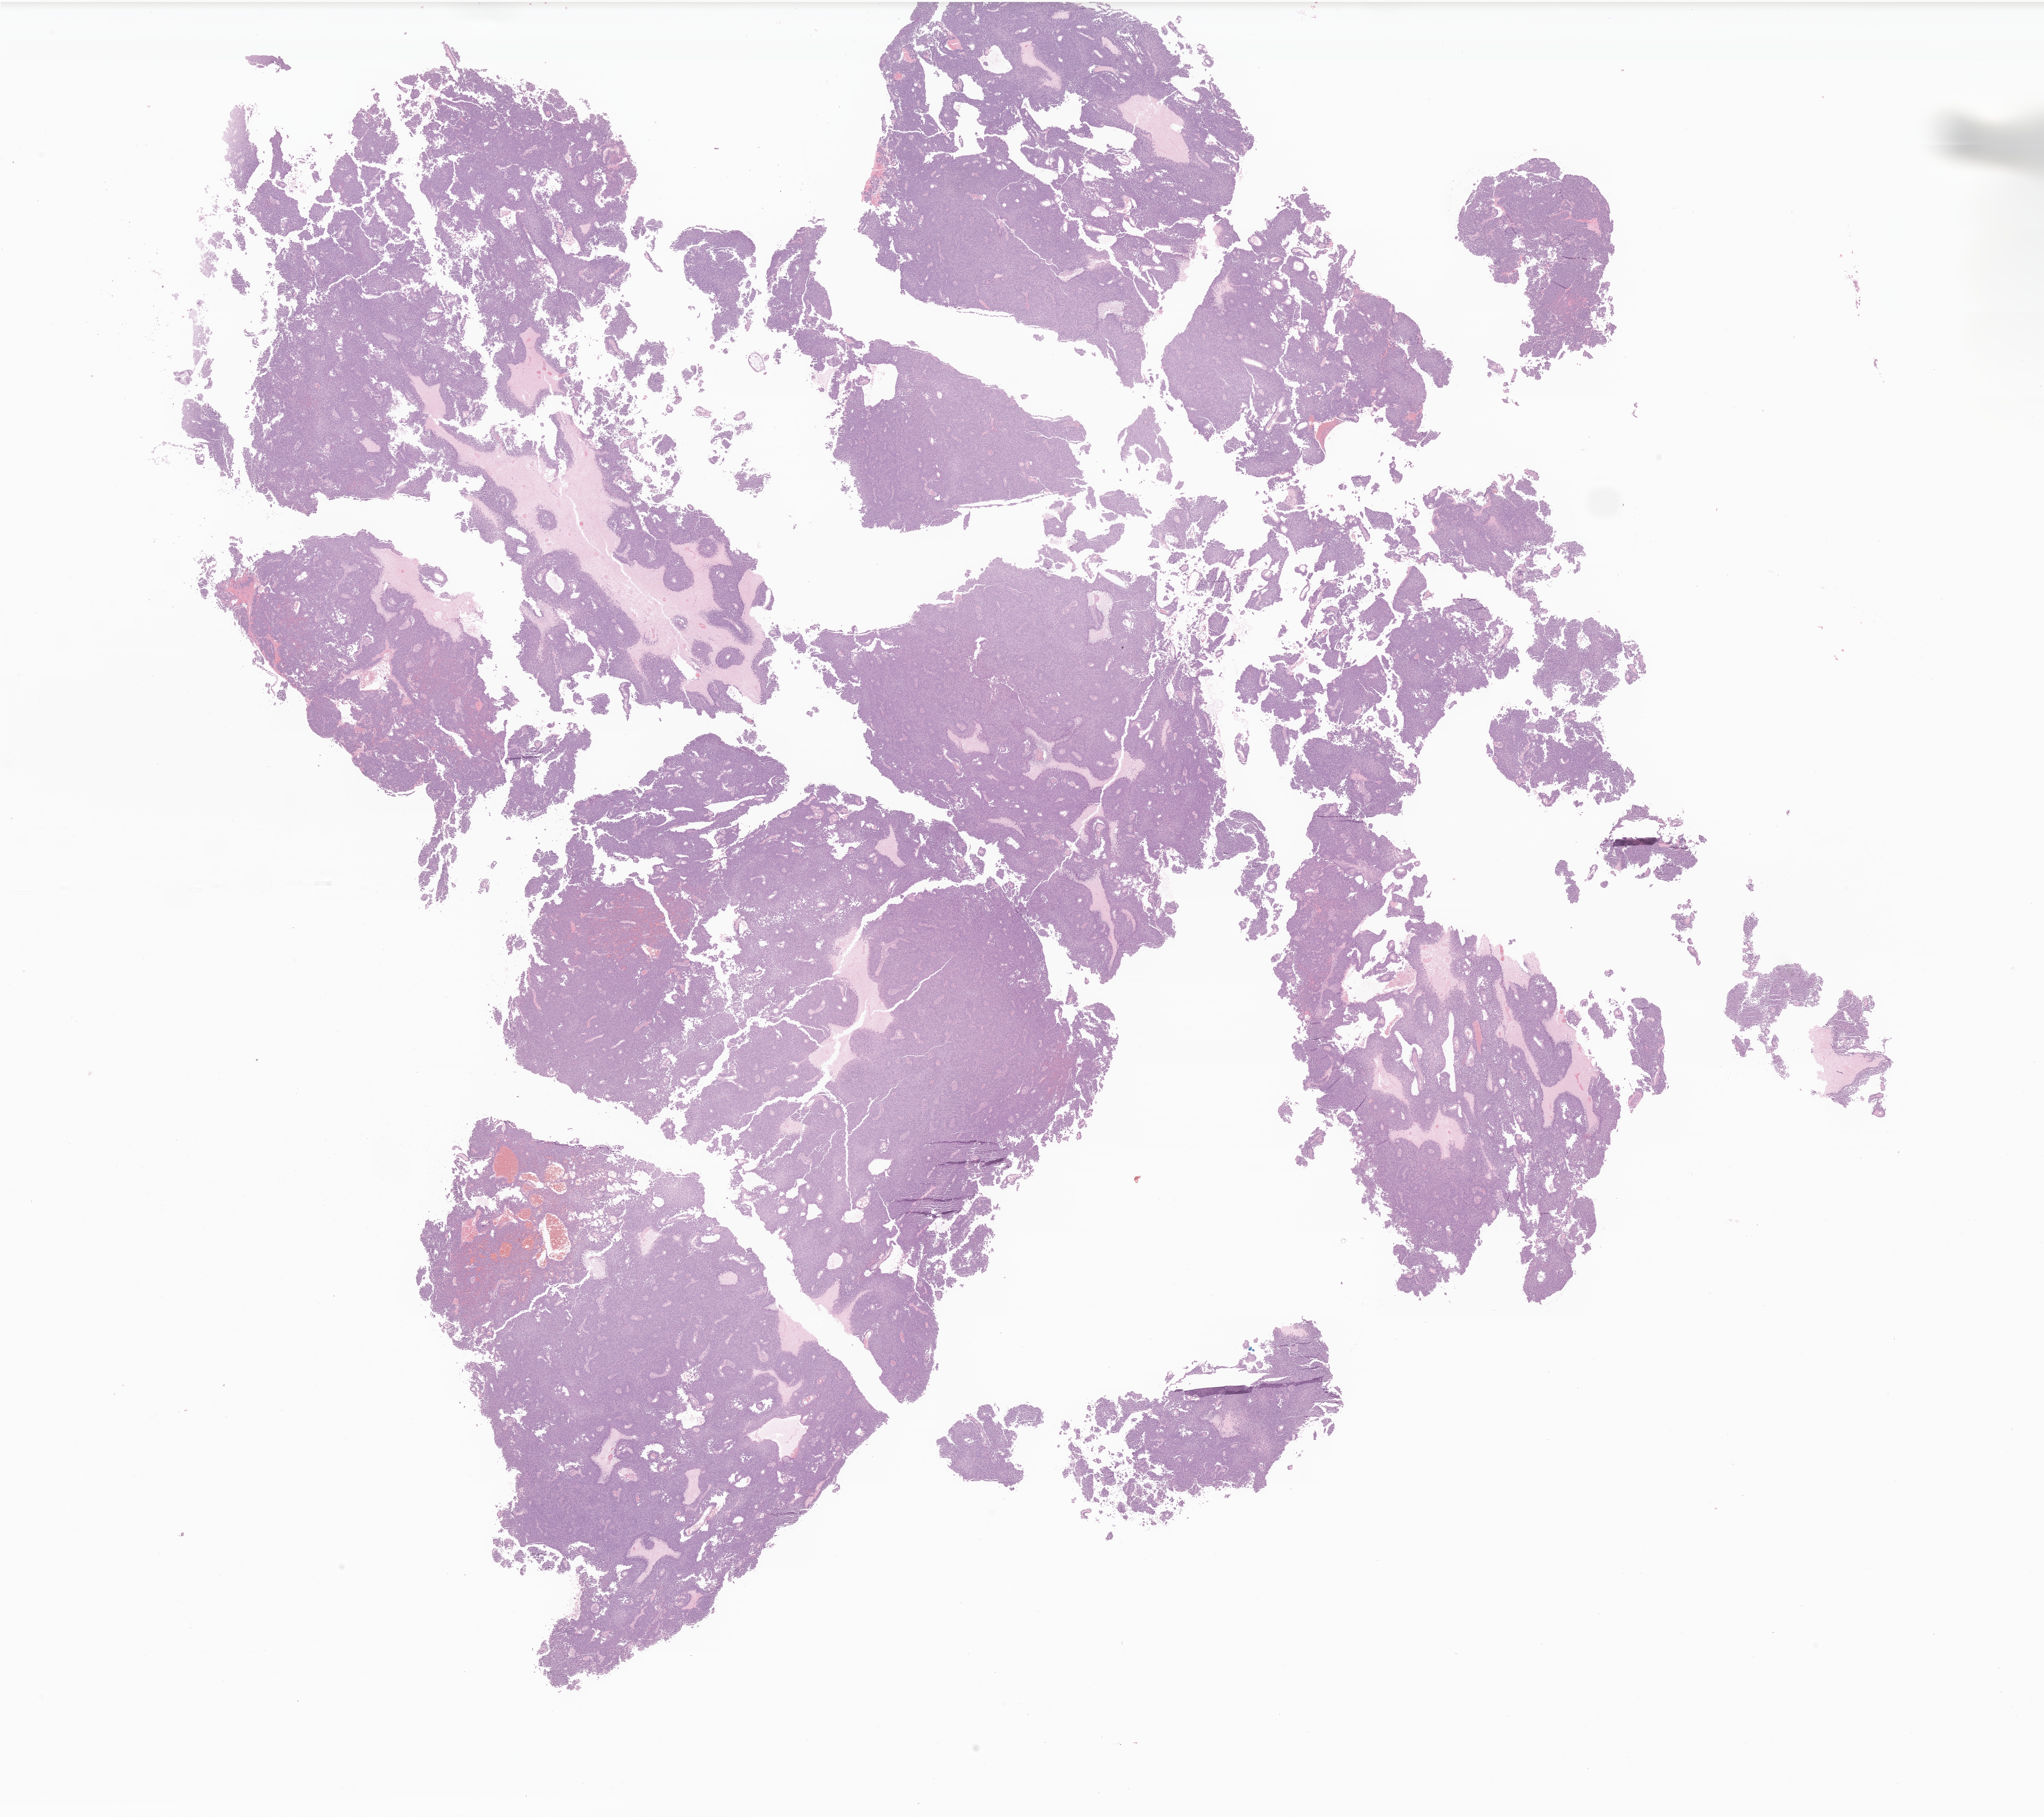
Haematoxylin and eosin whole-slide image of tumor tissue from the head and neck — low-resolution overview of the scanned area, about 26.1 x 23.2 mm. Patient: male, age 735 days.
Specimen: formalin-fixed, paraffin-embedded (FFPE) tissue.